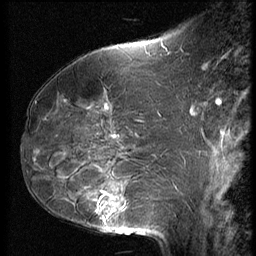
Breast MRI (dynamic contrast-enhanced), one sagittal slice; slice 26 of 62 in the series (ordered by position); 3 images stored at this slice position (order not interpretable as contrast timing); 1.5 T; TE 4.2 ms, TR 9 ms; 2.5 mm slice thickness; 256 × 256 image matrix, field of view 180 × 180 mm. Female patient, age 50 years. From the clinical record (not read from this slice): setting: breast cancer imaged before/during neoadjuvant chemotherapy; receptor status: HR-positive, HER2-negative.
Structures marked on this image (semi-automatically segmented with operator editing):
- analysis volume of interest (the breast-tissue region the enhancement analysis was run in; not a lesion): bounding box (x1, y1, x2, y2) in pixels: (59, 125, 139, 237)
- tumour enhancement mask (voxels above the 140 % enhancement threshold inside the analysis volume of interest): (96, 193, 109, 220)